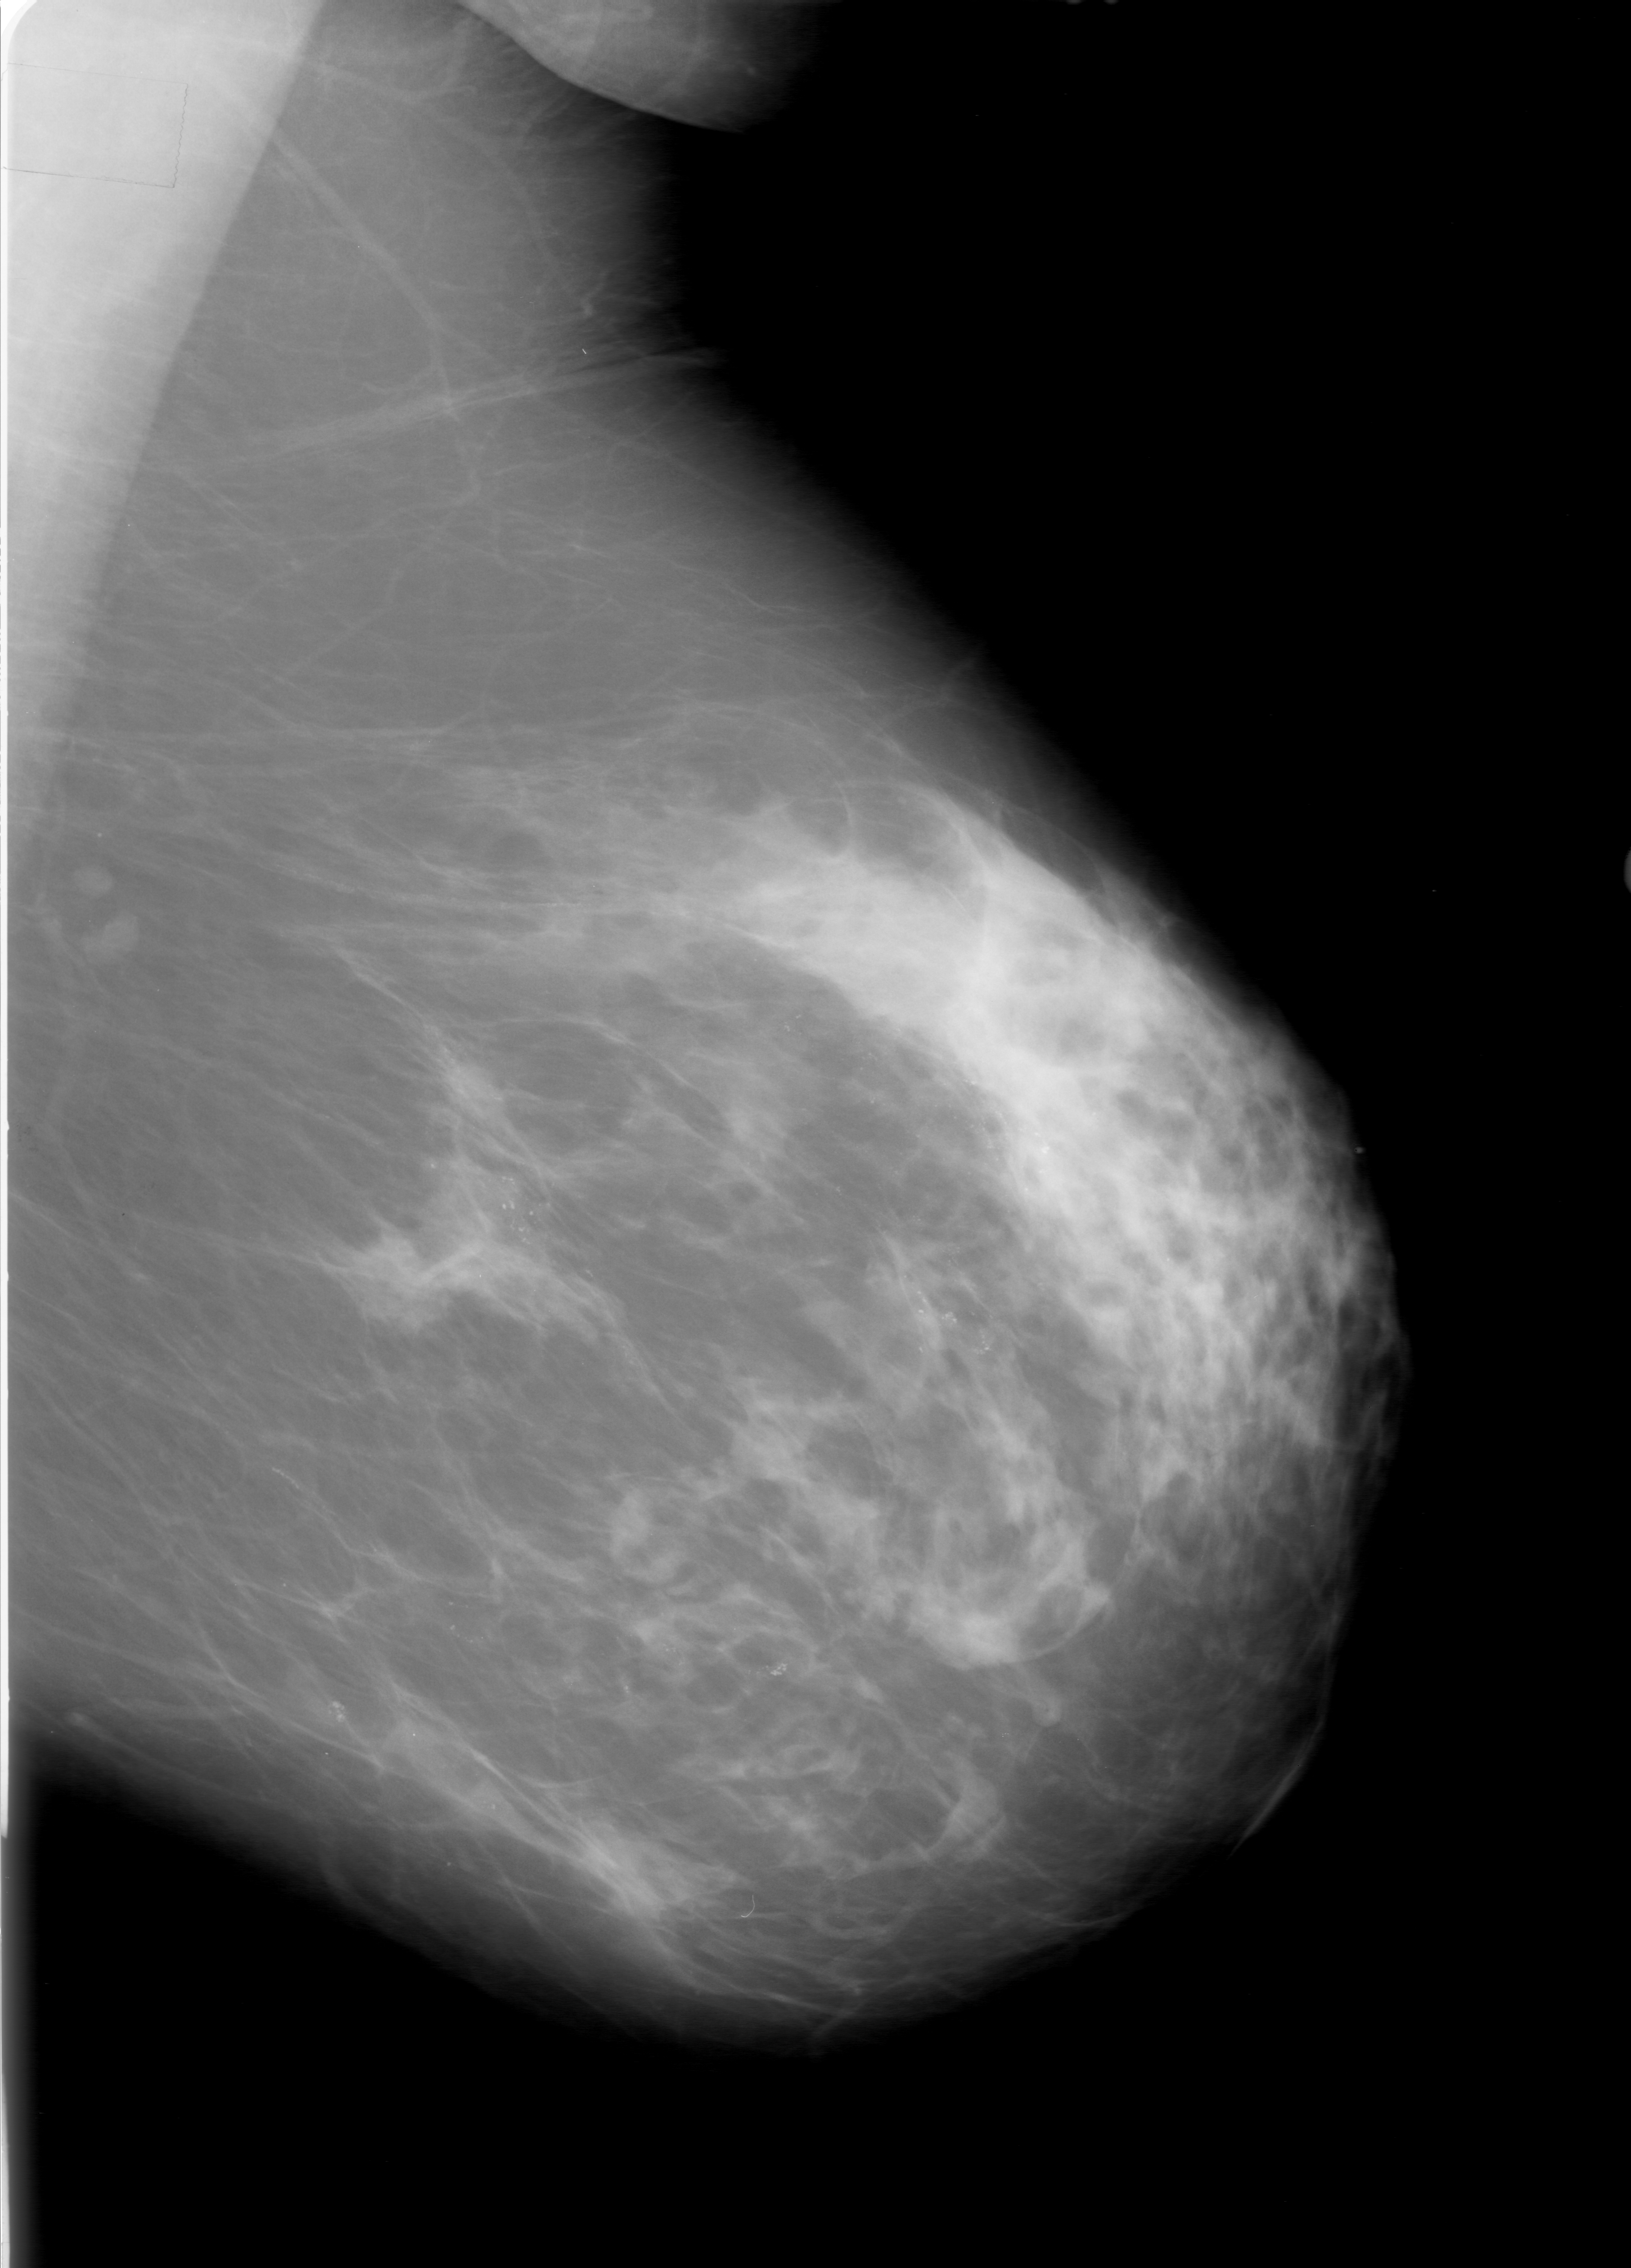
Scanned film-screen mammogram; left breast; MLO view; breast composition: heterogeneously dense (BI-RADS density category 3 of 4).
Marked findings (only marked abnormalities are described; nothing is implied about the rest of the image): calcifications, morphology pleomorphic, distribution regional; BI-RADS assessment category 5; subtlety rating 5 on a 1 (subtle) to 5 (obvious) scale; pathology result (as recorded, not read from the image): malignant.